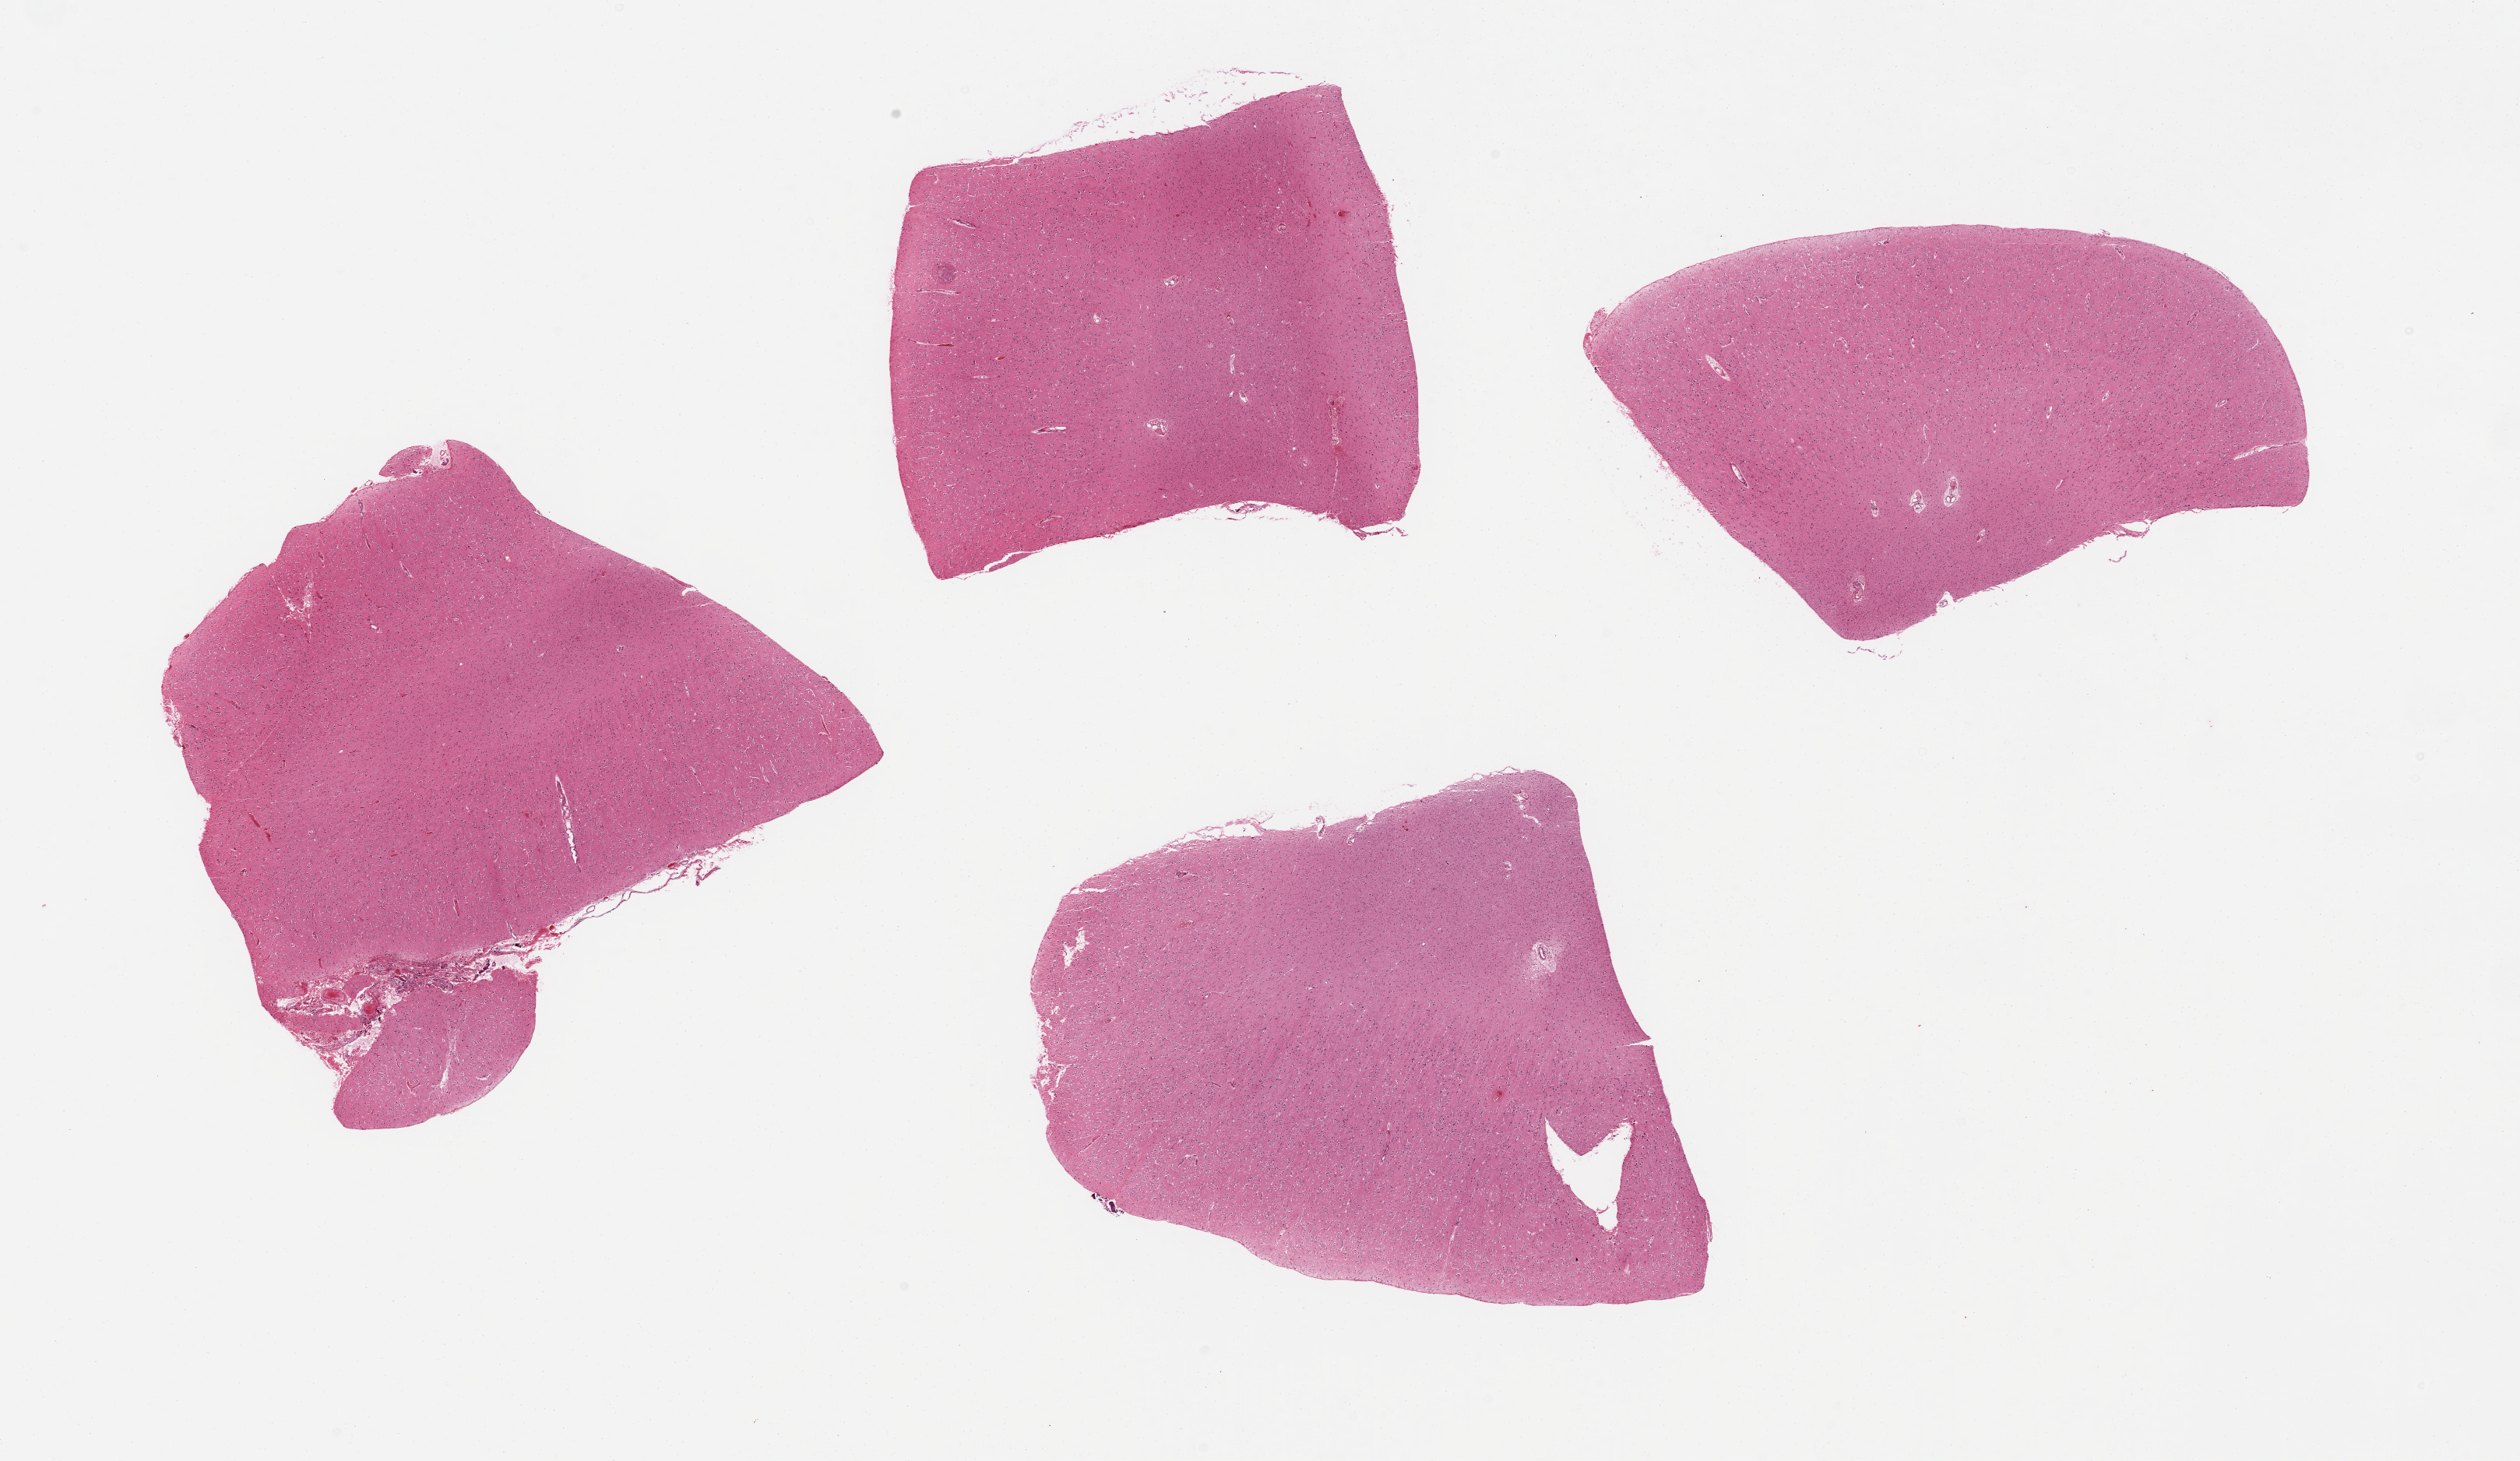
Hematoxylin and eosin (H&E) whole-slide image — whole scanned area (about 25.6 x 14.8 mm, from a 20x scan) shown as a low-resolution overview; PAXgene-fixed paraffin-embedded (PFPE) section; target tissue: cerebral cortex; donor tissue sample. Donor sex: male.
- reviewer comment on this tissue sample: 4 pieces